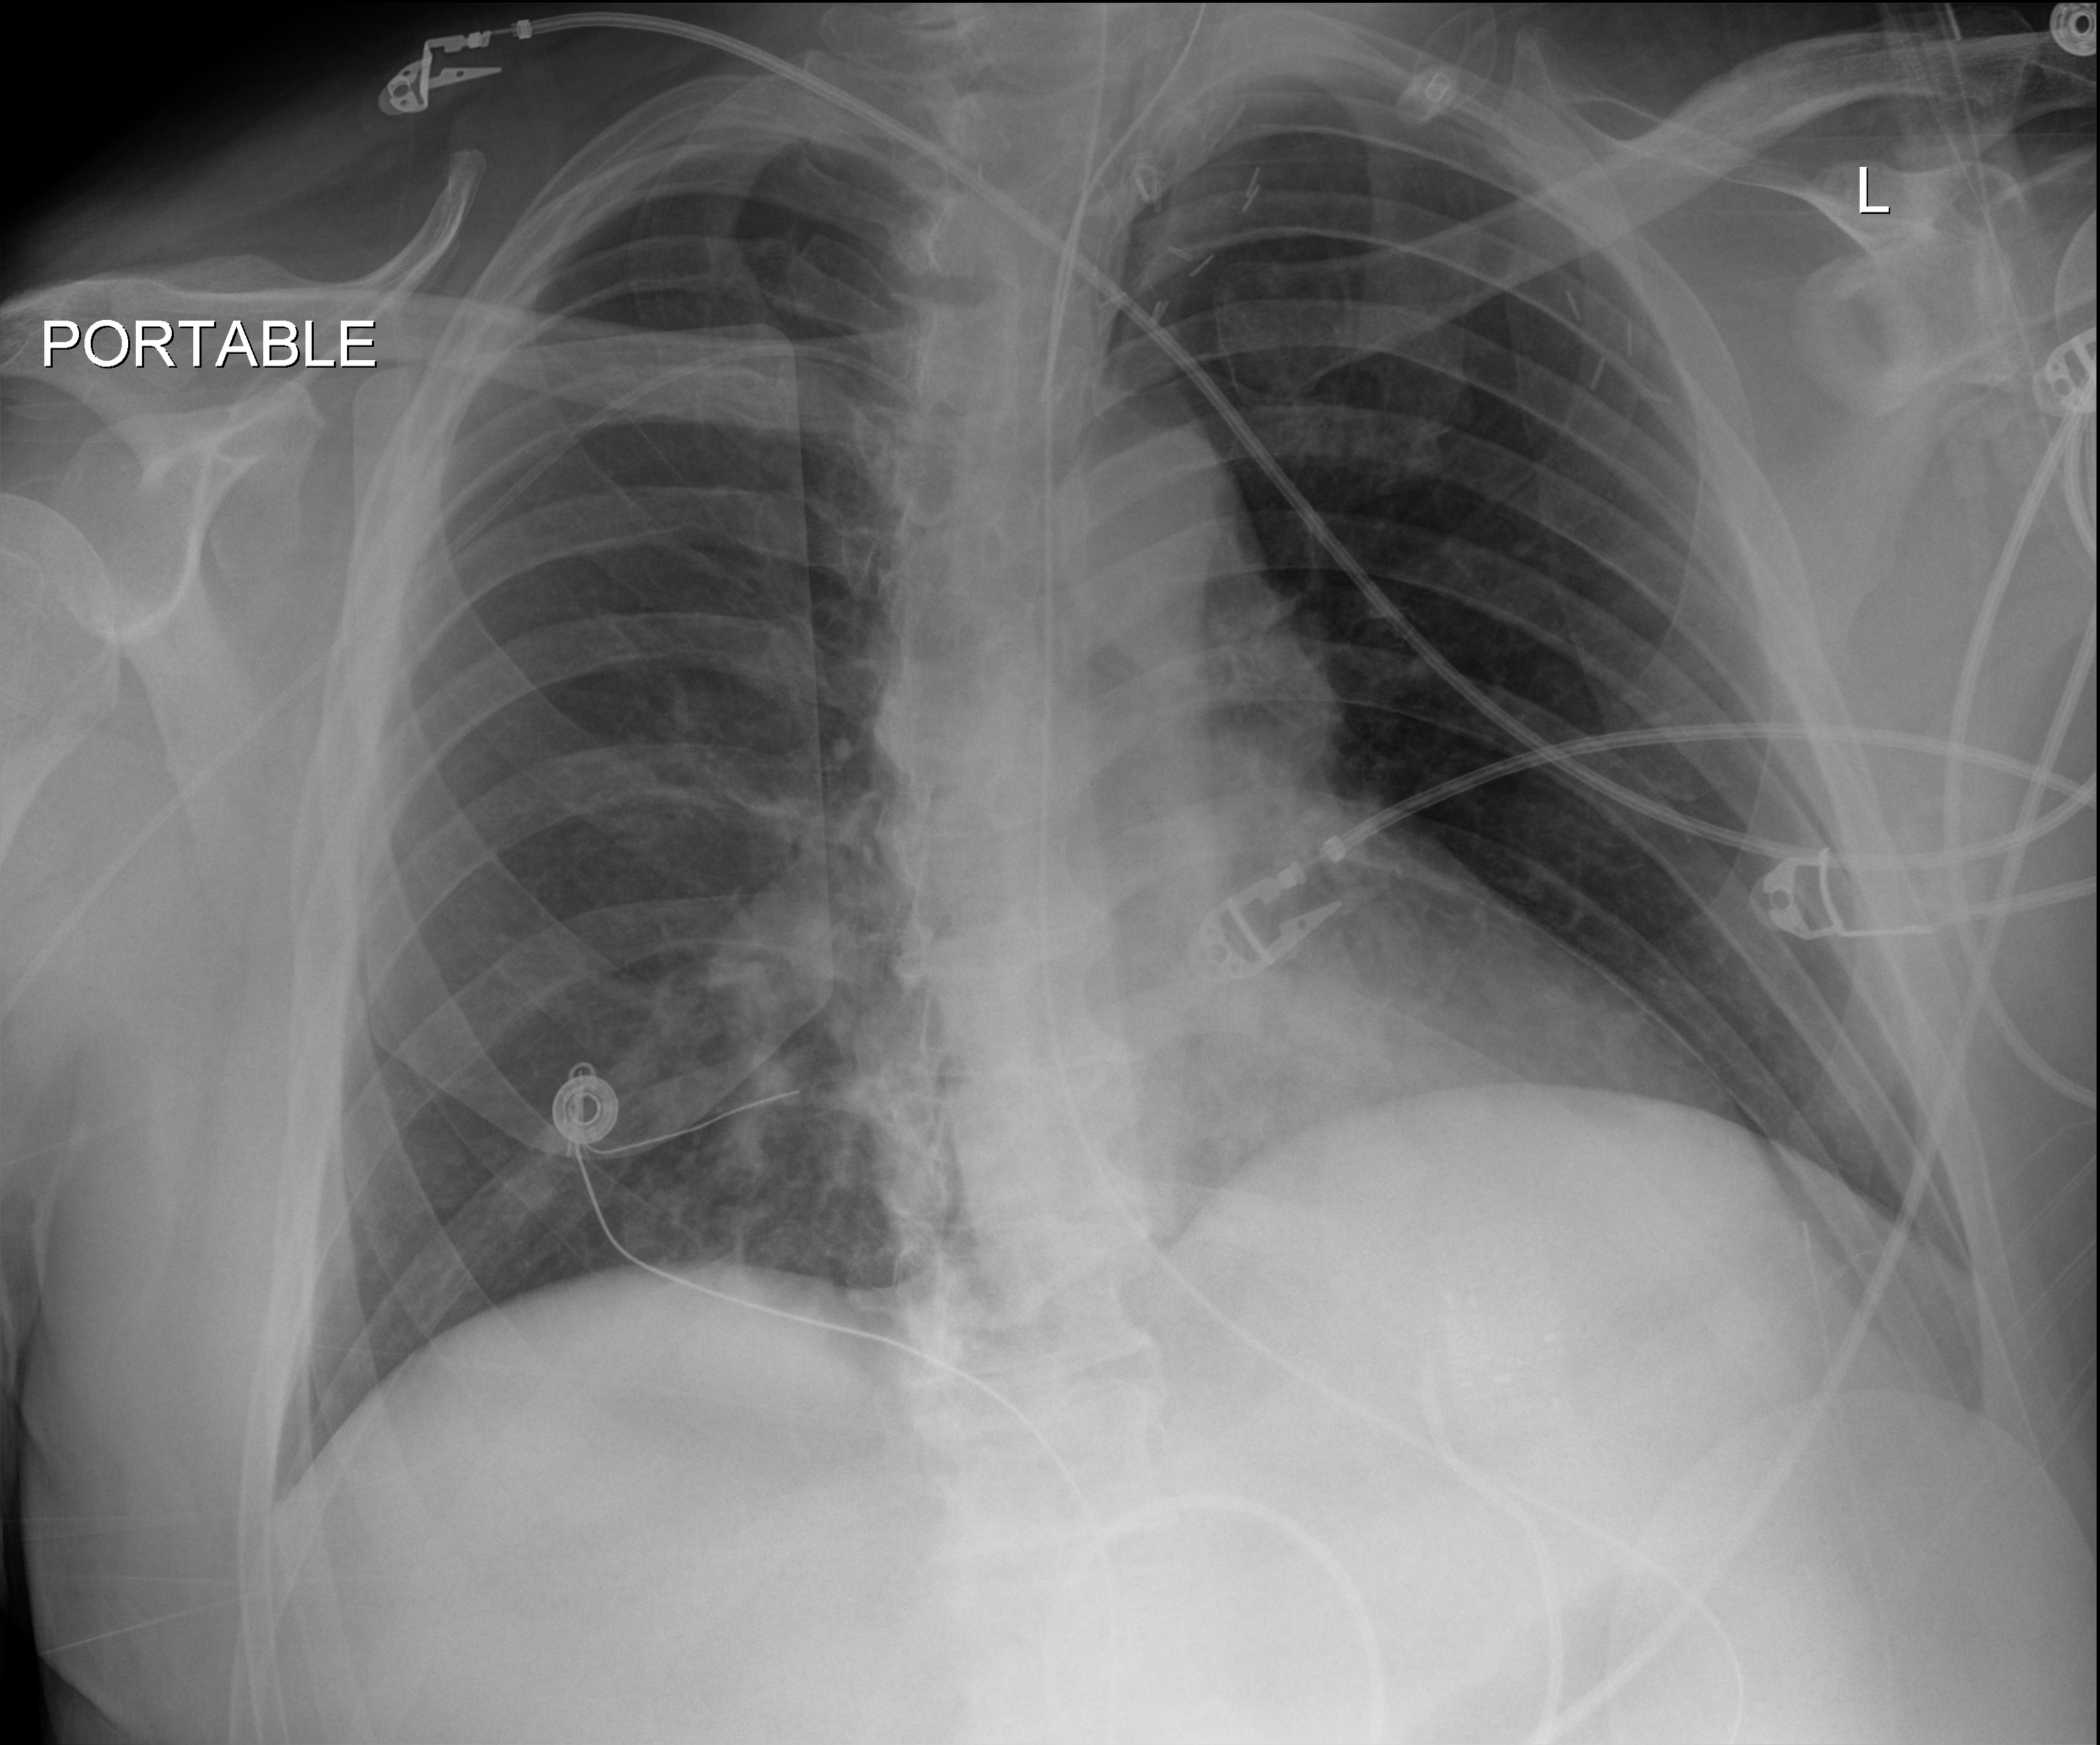
Bedside chest radiograph (digital radiography); anteroposterior (AP) projection. Patient hospitalised with COVID-19, aged 18–59 years.
Admission-level facts for this patient (not findings on this image; timing relative to this image not recorded): chronic kidney disease (admission record): yes; mechanically ventilated during this hospital stay: yes.